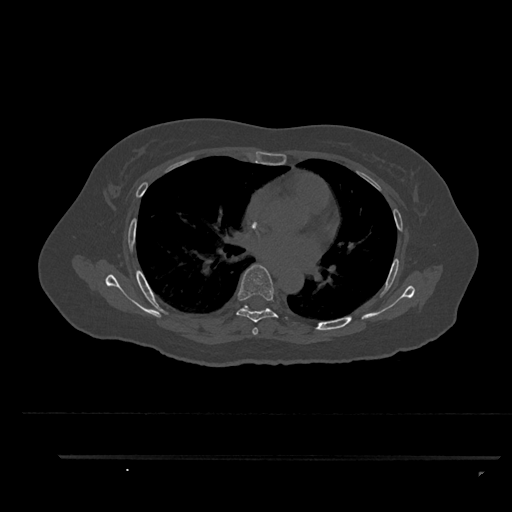
CT including the spine, one axial slice. Slice 556 of 797 in the series (ordered by position). Bone window (W 1800 / L 400 HU). 512 × 512 image matrix, field of view 408 × 408 mm. Patient: female, 44 years. From the clinical record (not read from this slice): primary cancer: renal.
Outlined on this slice (semi-automatic segmentation, software-assisted and operator-edited):
- T5 vertebra: box from (x=253, y=328) to (x=258, y=334) px
- T6 vertebra: (x=236, y=264)–(x=287, y=335)